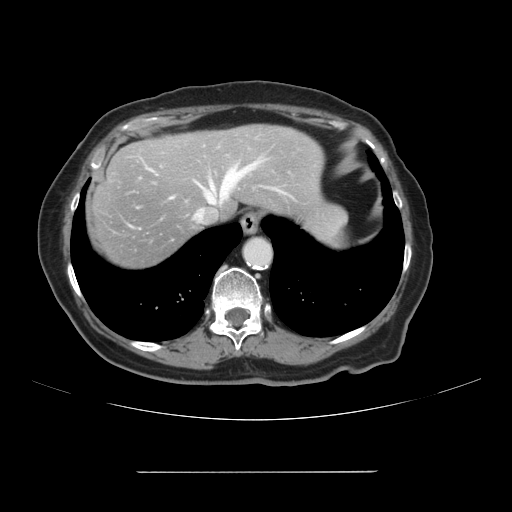
Contrast-enhanced abdominal CT, one axial slice; position 92 of 111 along the scan axis; 120 kVp; intravenous contrast given; soft-tissue window (W 400 / L 40 HU); 2.5 mm slice thickness; 512 × 512 image matrix, field of view 400 × 400 mm. Female patient, age 74 years. Case-level facts recorded for this patient, not image findings: diagnosis: colorectal cancer liver metastases, imaged before liver resection; multiple liver metastases: yes; largest metastasis: 1.1 cm.
Structures marked on this image (outlined manually by an expert reader):
- hepatic veins: box from (x=195, y=164) to (x=258, y=220) px
- liver: (x=90, y=124)–(x=329, y=270)
- planned liver remnant (the part of the liver to remain after resection): (x=175, y=124)–(x=324, y=214)
- portal vein (with intrahepatic branches): (x=208, y=186)–(x=220, y=200)
- liver metastasis: (x=111, y=174)–(x=117, y=179)